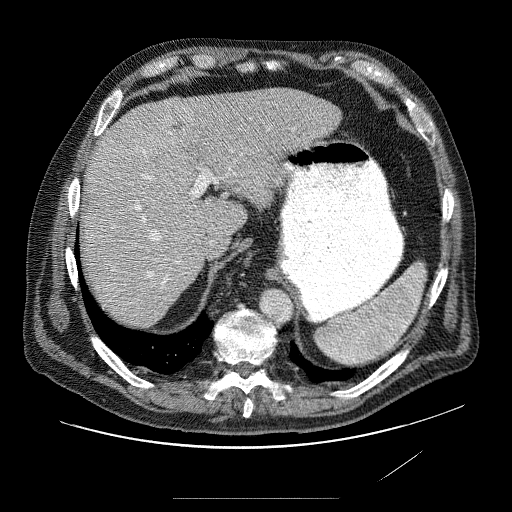
Contrast-enhanced abdominal CT (liver protocol), one axial slice. Slice 58 of 89 in the series (ordered by position). Reconstruction kernel STANDARD. 120 kVp. Soft-tissue window (W 400 / L 40 HU). 2.5 mm slice thickness. 512 × 512 image matrix, field of view 420 × 420 mm. From the clinical record (not read from this slice): diagnosis: hepatocellular carcinoma (patient treated with transarterial chemoembolisation; whether this scan precedes or follows treatment is not stated here); TNM stage (as recorded): Stage-IVA; Child-Pugh class: A; tumour differentiation: moderately differentiated; tumour nodularity: multinodular.
Outlined on this slice (semi-automatically segmented with operator editing):
- liver parenchyma outside the tumour (the mass and vessels are separate outlines, so this box may not span the whole liver): bounding box [x1, y1, x2, y2] px = [84, 88, 344, 308]
- mass: [96, 102, 272, 292]
- liver vessels: [119, 110, 304, 287]